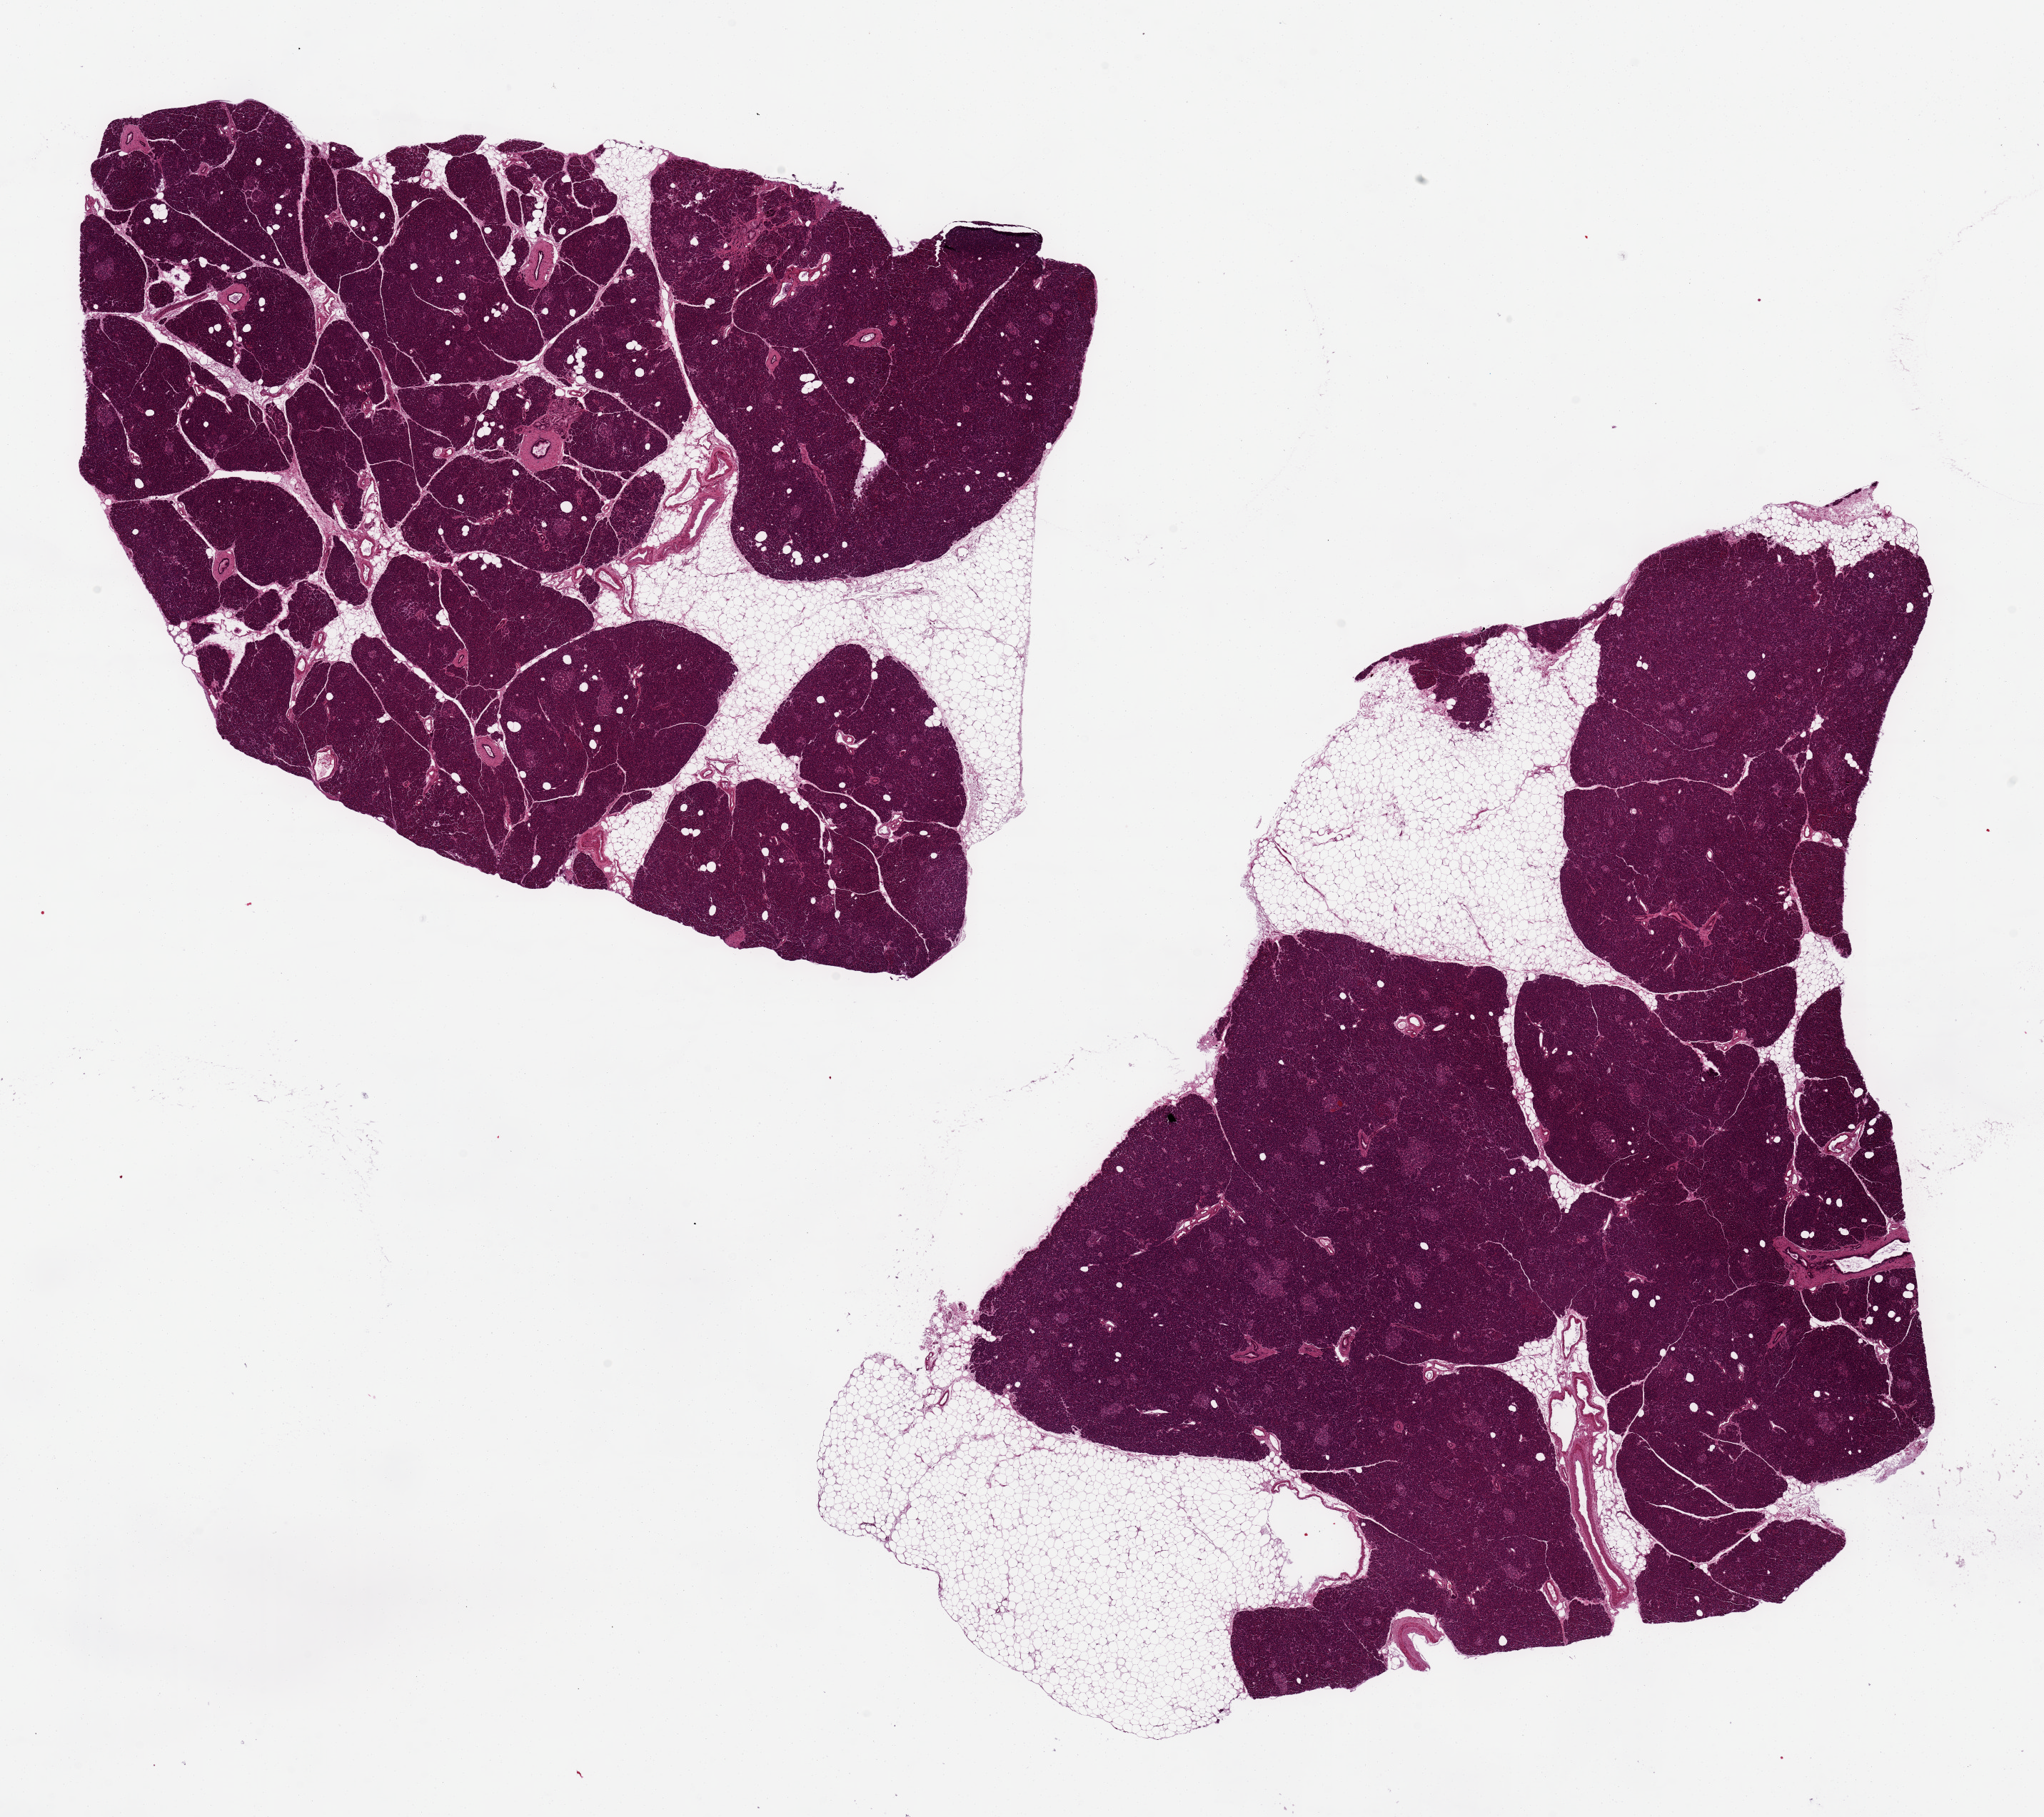
Whole-slide image, haematoxylin and eosin stain, brightfield, whole scanned area (about 22.6 x 20.1 mm) shown as a low-resolution overview; PAXgene-fixed paraffin-embedded (PFPE) section; target tissue: pancreas; donor tissue sample. Donor sex: male.
Review note (as recorded): 2 ~14x8mm aliquots, relatively clean, 5x2mm nodule of fat on end of one aliquot.